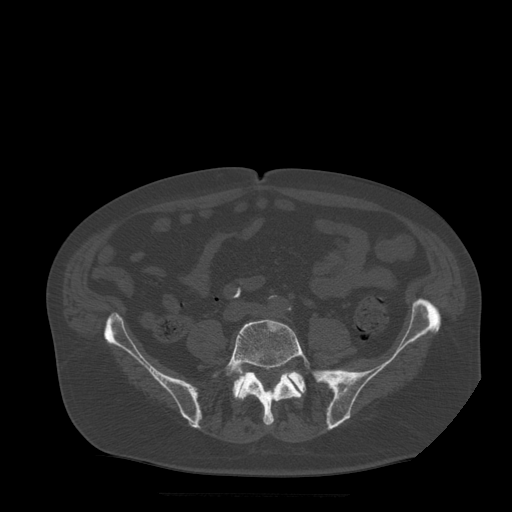
CT including the spine, one axial slice; position 86 of 522 along the scan axis; bone window (W 1800 / L 400 HU); 1.25 mm slice thickness; 512 × 512 image matrix, field of view 420 × 420 mm. Patient age 72 years. Case-level facts recorded for this patient, not image findings: primary cancer: prostate.
Structures marked on this image (semi-automatically segmented with operator editing):
- L5 vertebra: bounding box [x1, y1, x2, y2] px = [213, 320, 323, 426]